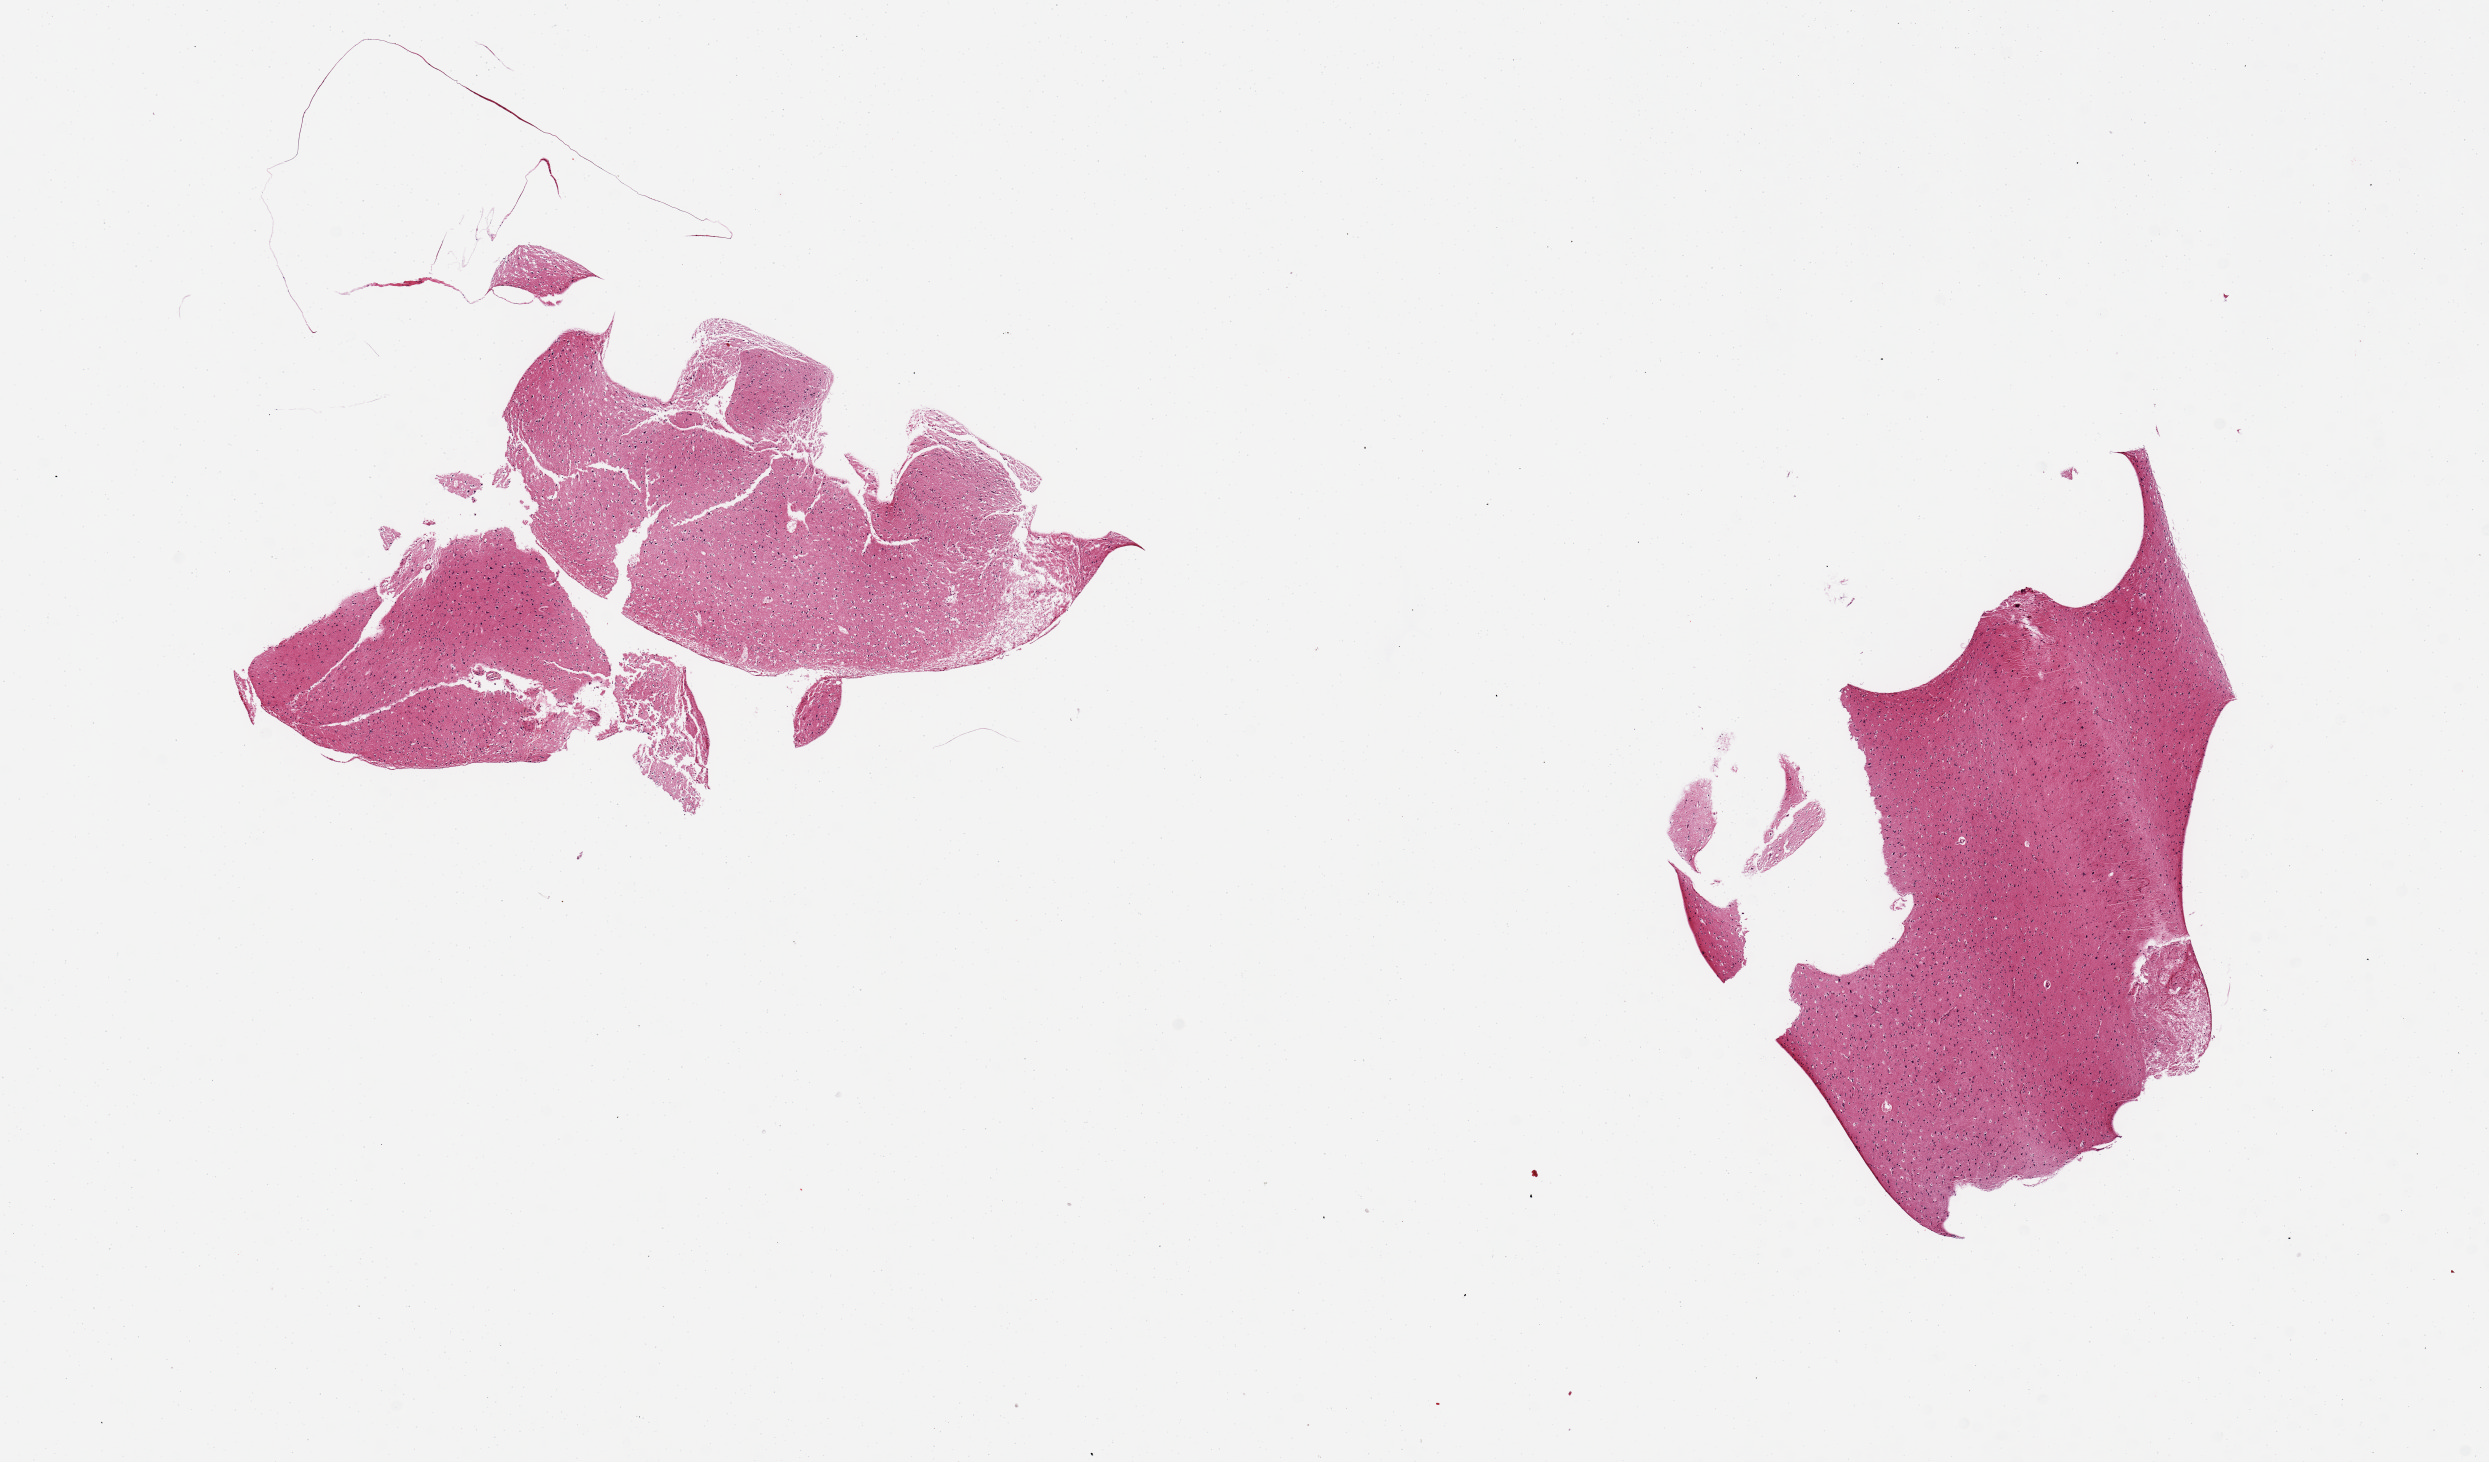
Haematoxylin and eosin whole-slide image — low-resolution overview of the scanned area, about 19.7 x 11.6 mm (acquisition: 20x scan). PAXgene-fixed paraffin-embedded (PFPE) section. Target tissue: cerebral cortex. Tissue donor sample. Donor sex: male.
Pathologist's review note for this sample: 2 pieces.